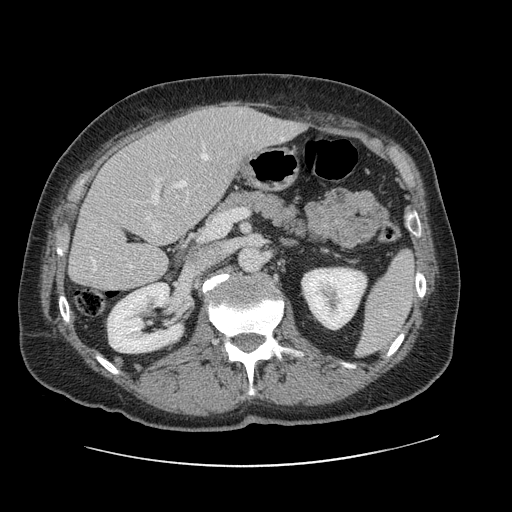
Contrast-enhanced abdominal CT, one axial slice. Soft-tissue window (W 400 / L 40 HU). 512 × 512 image matrix, field of view 402 × 402 mm. Male patient, age 71 years. From the clinical record (not read from this slice): diagnosis: colorectal cancer liver metastases, imaged before liver resection; multiple liver metastases: no; largest metastasis: 3.3 cm; chemotherapy before resection: no.
Annotated regions visible in this slice (expert manual segmentation):
- hepatic veins: bounding box <93,154,227,271> (left, top, right, bottom; pixels)
- liver: <70,103,300,292>
- planned liver remnant (the part of the liver to remain after resection): <70,141,198,292>
- portal vein (with intrahepatic branches): <151,178,163,205>